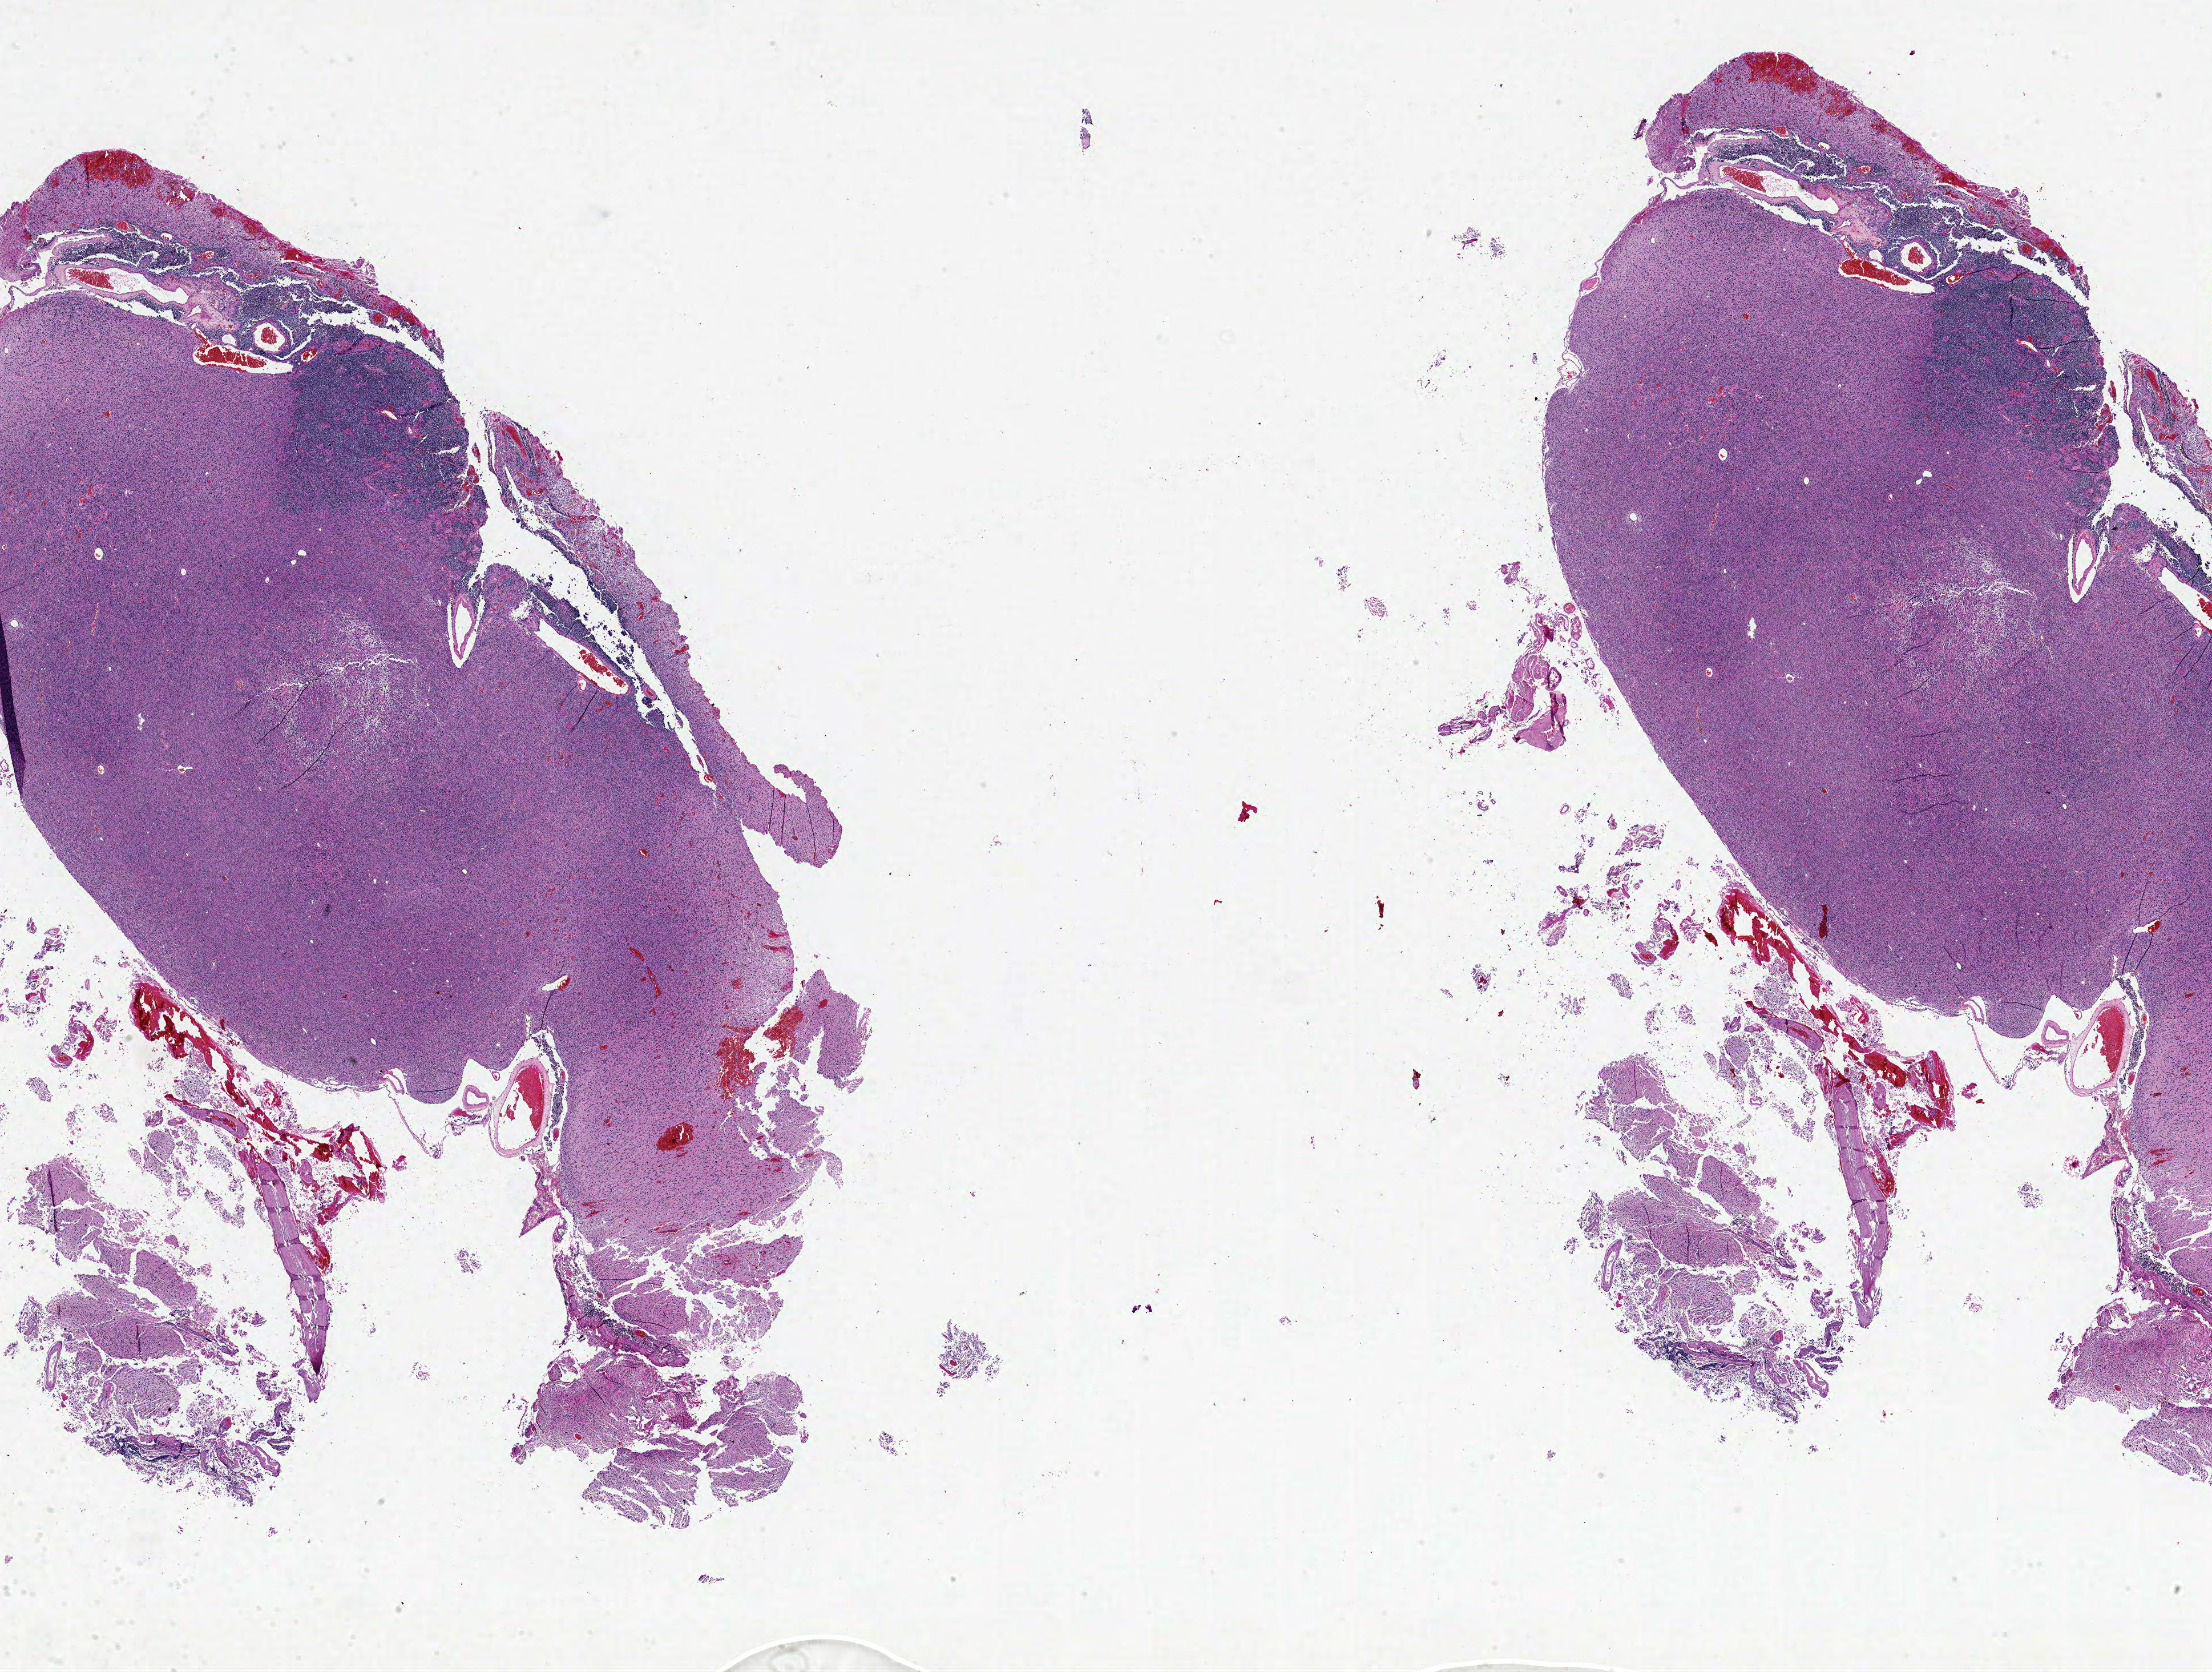
Whole-slide histology image, H&E — whole scanned area (about 31.0 x 23.4 mm, acquisition: 20x scan) shown as a low-resolution overview; formalin-fixed paraffin-embedded (FFPE) diagnostic section; brain, primary tumour sample. Female patient; age at initial diagnosis 75 years.
Pathologic diagnosis: Glioblastoma.